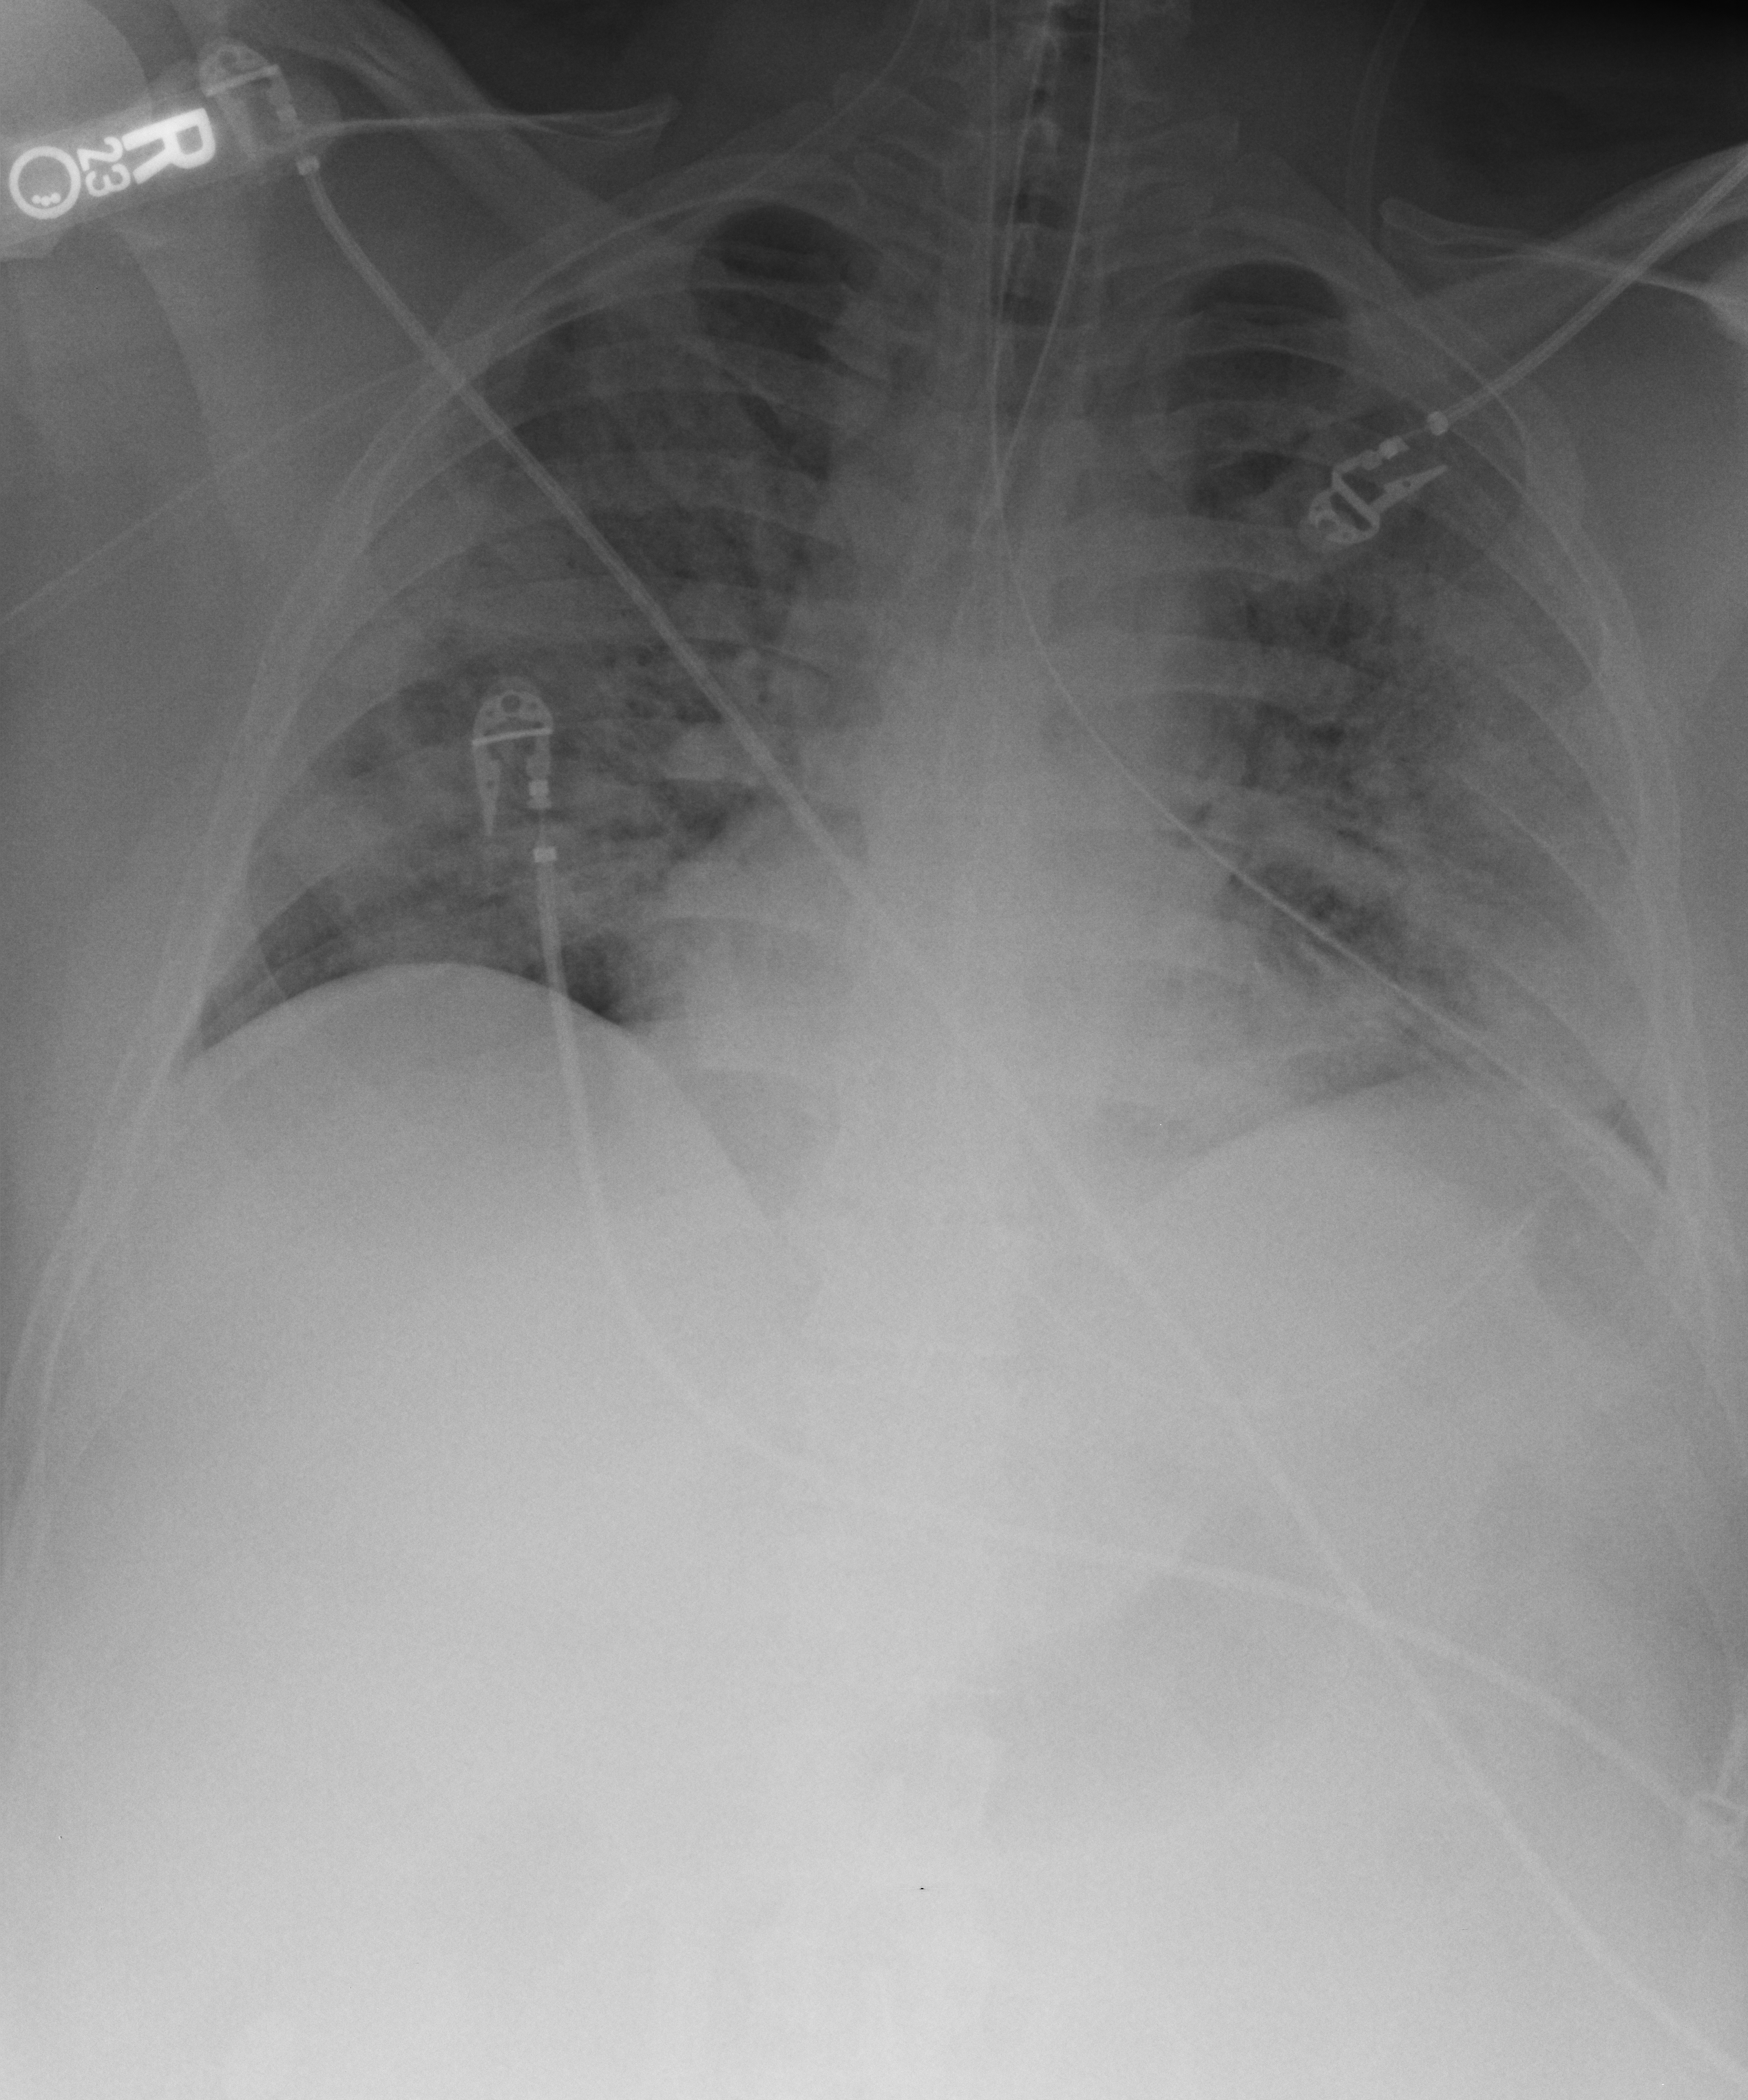
Portable chest radiograph; anteroposterior (AP) projection. Adult patient hospitalised with COVID-19, age 18–59 years.
From the hospital-stay record, not from the radiograph (when in the stay this image was taken is not recorded): diabetes (admission record): no; mechanically ventilated during this hospital stay: yes; admitted to intensive care during this hospital stay: yes.